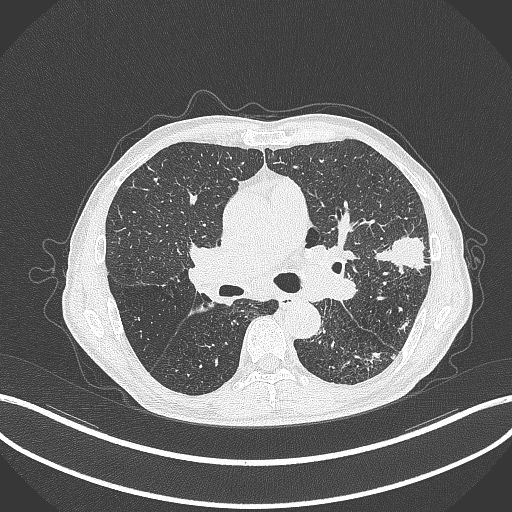
Chest CT, one axial slice. Reconstruction kernel B70f. 120 kVp. Lung window (W 1500 / L -600 HU). 1 mm slice thickness. 512 × 512 image matrix, field of view 400 × 400 mm. Male patient, age 74 years. From the clinical record (not read from this slice): clinical TNM (as recorded): T2a N1 M0.
Structures marked on this image (bounding box drawn by a radiologist):
- lung tumour (recorded histology: adenocarcinoma): bounding box (x1, y1, x2, y2) in pixels: (376, 232, 431, 273)